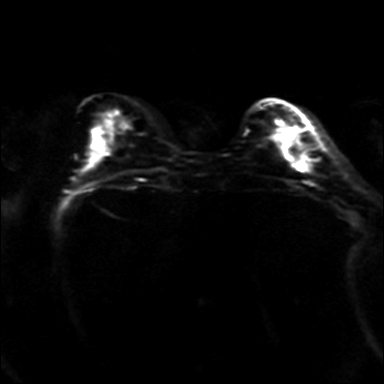
Breast MRI, one axial slice; slice 12 of 36 in the series (ordered by position); diffusion-weighted series; image 2 of 4 stored at this slice position (different b-values; order by instance number); 3 T; 384 × 384 image matrix. Female patient.
Structures marked on this image (outlined manually by an expert reader):
- tumour on diffusion-weighted imaging: bounding box [x1, y1, x2, y2] px = [290, 140, 300, 163]